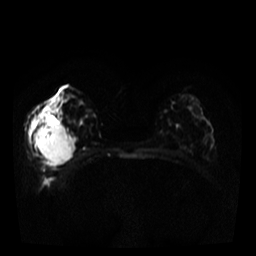
Breast MRI, one axial slice. Position 14 of 34 along the scan axis. Diffusion-weighted series; image 2 of 4 stored at this slice position (different b-values; order by instance number). 3 T. 256 × 256 image matrix, field of view 320 × 320 mm. Female patient.
Structures marked on this image (manually delineated by an expert):
- tumour on diffusion-weighted imaging: box from (x=36, y=125) to (x=73, y=161) px